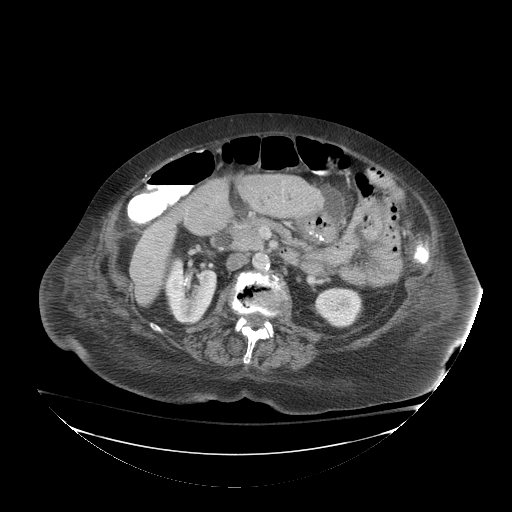
Contrast-enhanced abdominal CT (liver protocol), one axial slice. Slice 28 of 81 in the series (ordered by position). Reconstruction kernel STANDARD. Soft-tissue window (W 400 / L 40 HU). 2.5 mm slice thickness. 512 × 512 image matrix, field of view 500 × 500 mm. Case-level facts recorded for this patient, not image findings: diagnosis: hepatocellular carcinoma (patient treated with transarterial chemoembolisation; whether this scan precedes or follows treatment is not stated here); TNM stage (as recorded): Stage-I; Child-Pugh class: B; tumour nodularity: uninodular.
Annotated regions visible in this slice (semi-automatic segmentation, software-assisted and operator-edited):
- liver parenchyma outside the tumour (the mass and vessels are separate outlines, so this box may not span the whole liver): box from (x=130, y=215) to (x=176, y=304) px